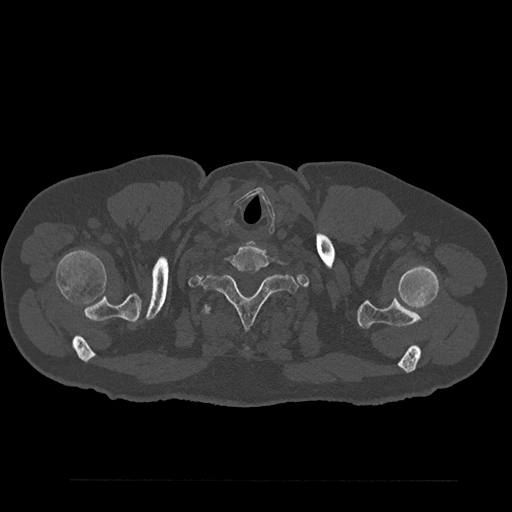
CT including the spine, one axial slice. Slice 755 of 797 in the series (ordered by position). Reconstruction kernel Br40s/3. Bone window (W 1800 / L 400 HU). 0.5 mm slice thickness. 512 × 512 image matrix, field of view 430 × 430 mm. Male patient, age 61 years. From the clinical record (not read from this slice): primary cancer: prostate.
Structures marked on this image (semi-automatically segmented with operator editing):
- T1 vertebra: box from (x=202, y=274) to (x=298, y=328) px
- T2 vertebra: (x=201, y=303)–(x=294, y=351)